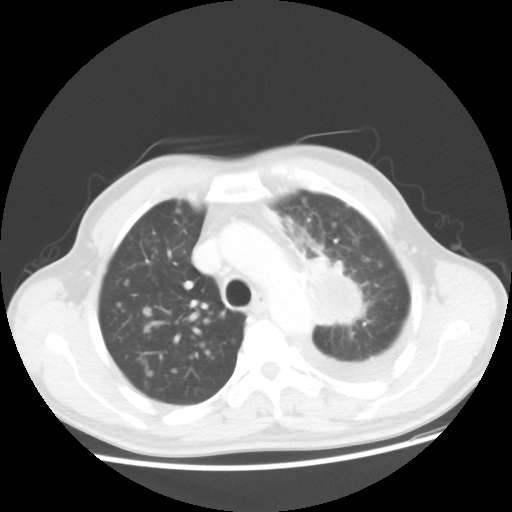
Chest CT, one axial slice. Position 35 of 48 along the scan axis. Reconstruction kernel STANDARD. Lung window (W 1500 / L -600 HU). 5 mm slice thickness. 512 × 512 image matrix, field of view 362 × 362 mm. Patient: male, 55 years. From the clinical record (not read from this slice): clinical TNM (as recorded): T2 N3 M1a; histopathological grade: G3.
Outlined on this slice (rectangle marked by the reading radiologist):
- lung tumour (recorded histology: squamous cell carcinoma): bounding box <307,255,366,337> (left, top, right, bottom; pixels)